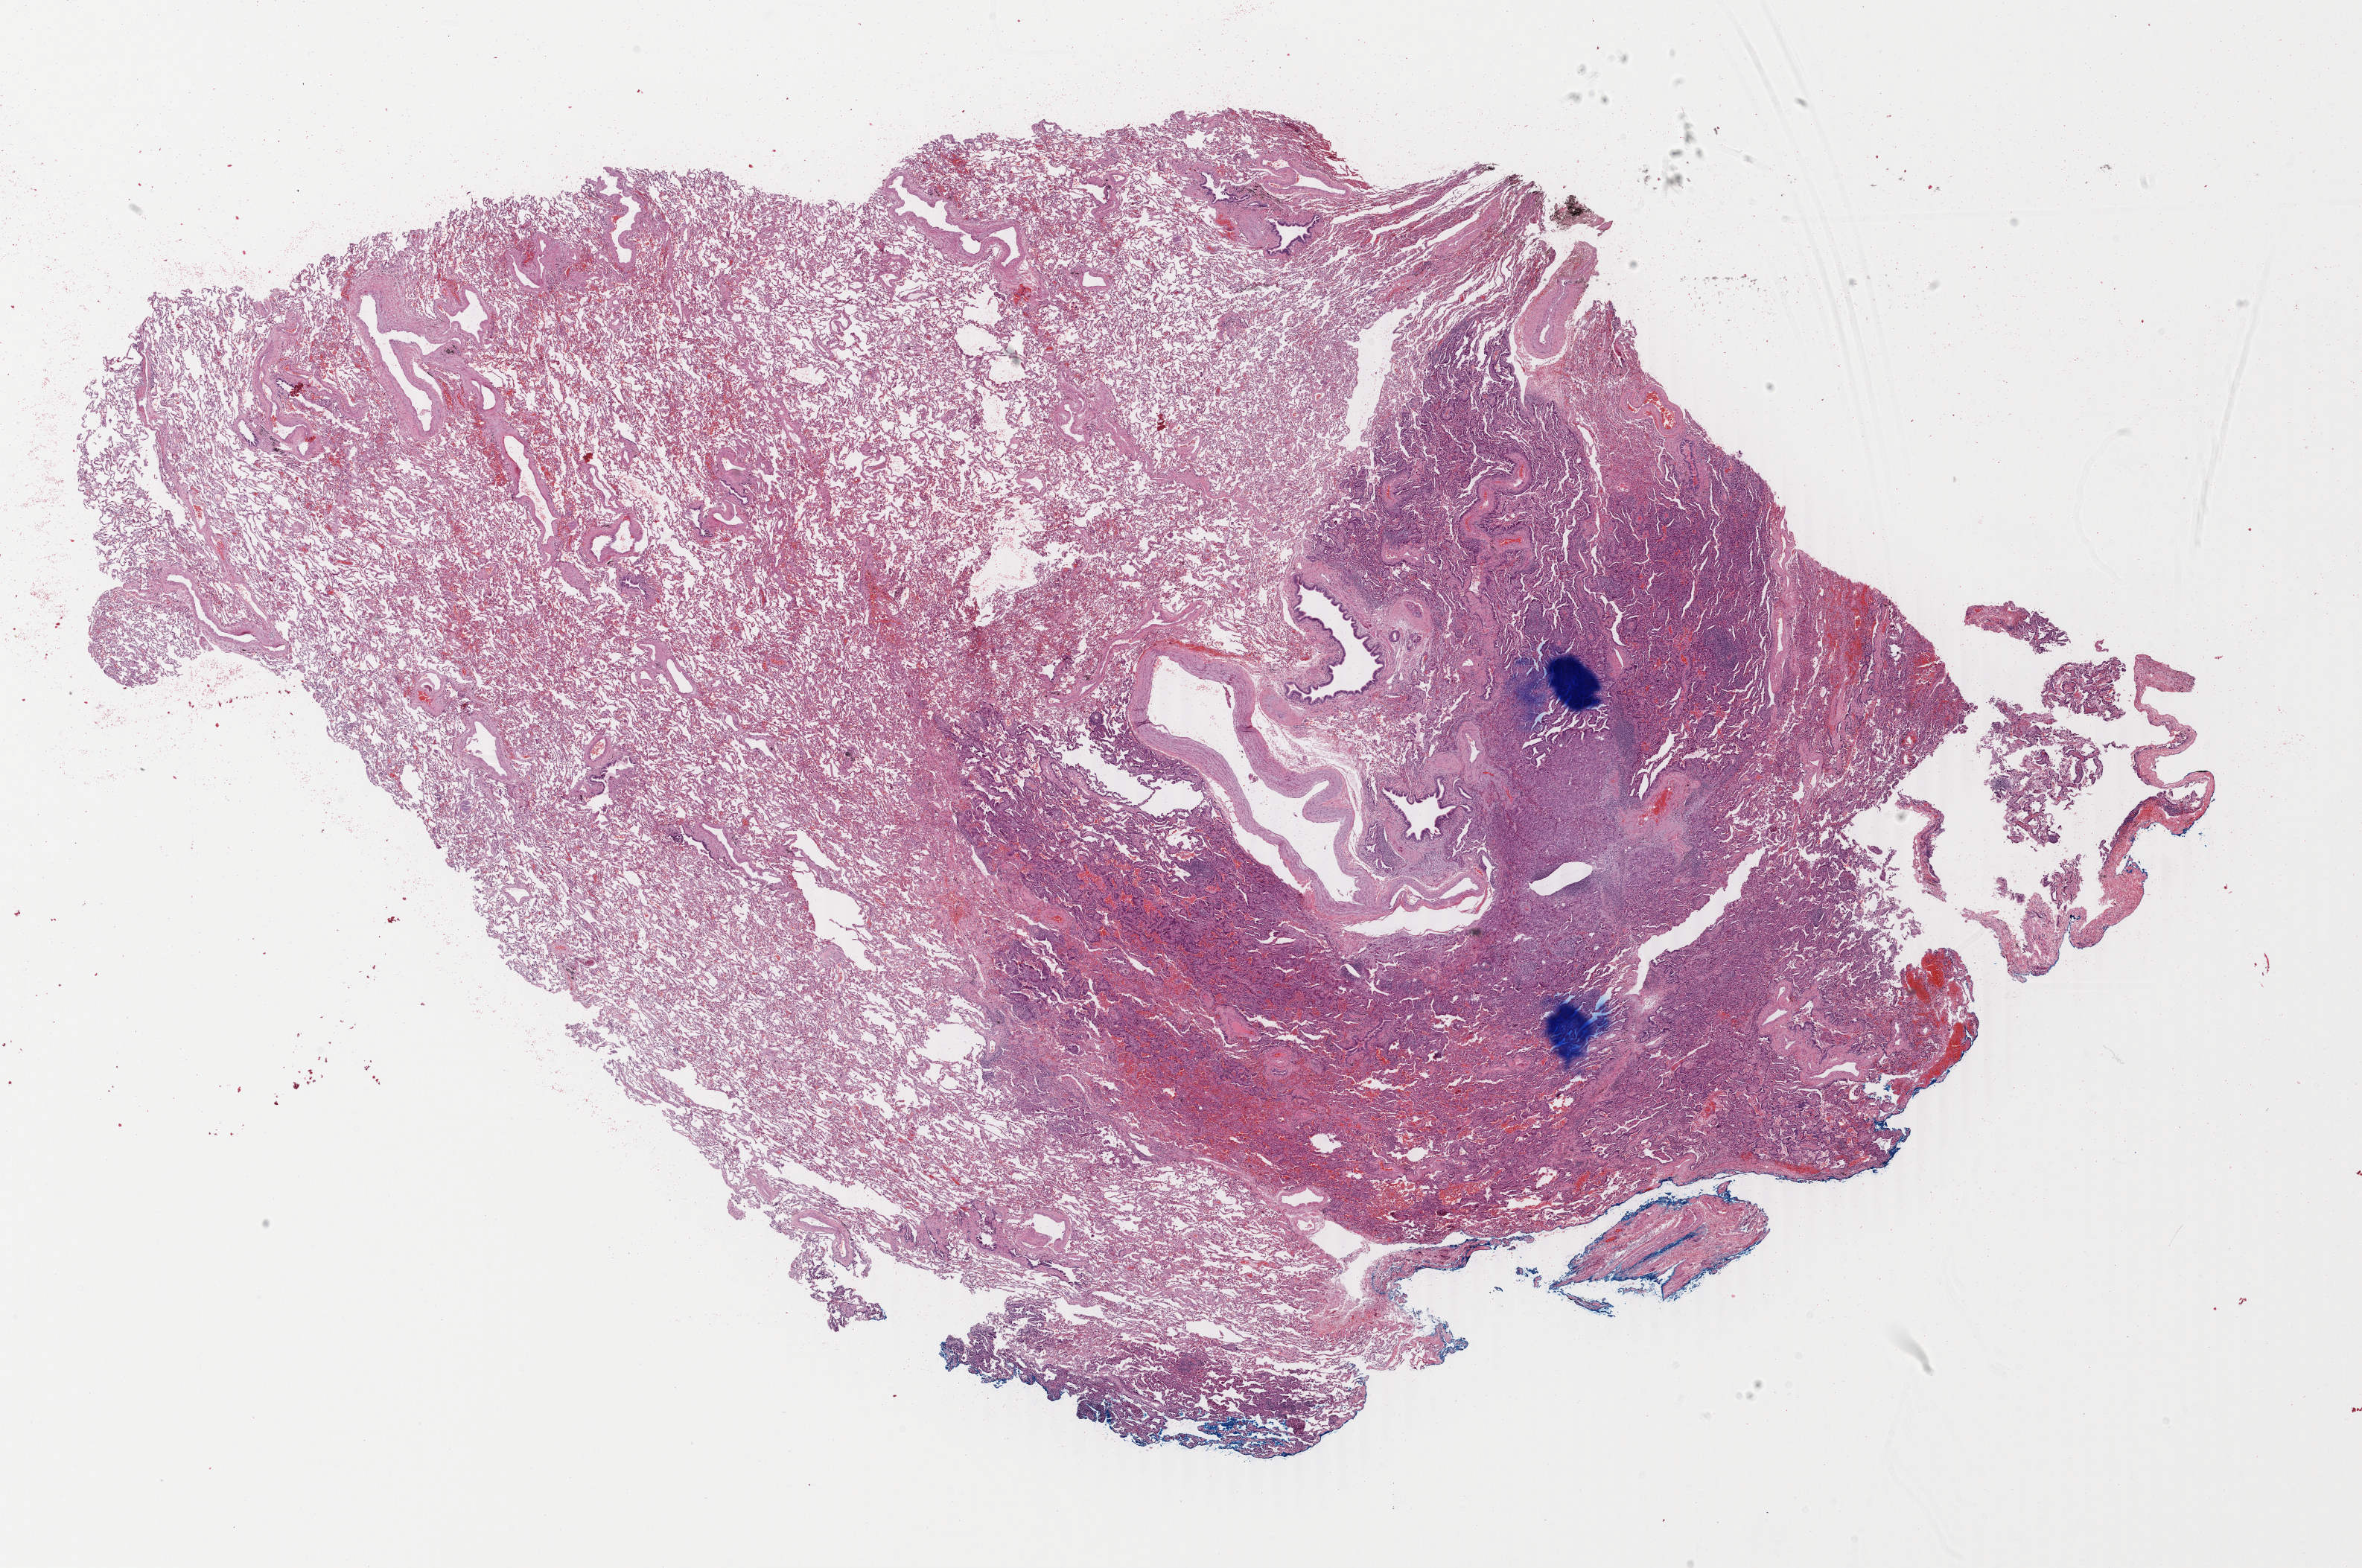
Digitized H&E-stained tissue section (whole slide) — shown as a low-resolution overview of the whole scanned area (about 25.2 x 16.7 mm), FFPE section, sample: primary tumour, lung. Female patient; age at initial diagnosis 77 years.
Pathologic diagnosis: Adenocarcinoma, NOS (upper lobe, lung).